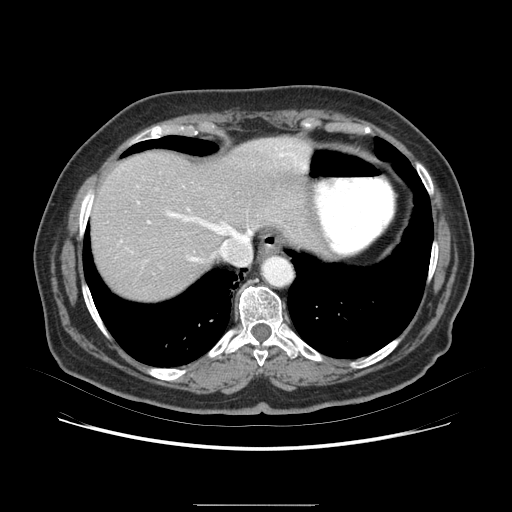
Contrast-enhanced abdominal CT (liver protocol), one axial slice; position 67 of 79 along the scan axis; 120 kVp; soft-tissue window (W 400 / L 40 HU); 2.5 mm slice thickness; 512 × 512 image matrix, field of view 380 × 380 mm. From the clinical record (not read from this slice): diagnosis: hepatocellular carcinoma (patient treated with transarterial chemoembolisation; whether this scan precedes or follows treatment is not stated here); TNM stage (as recorded): Stage-I; Child-Pugh class: A.
Structures marked on this image (semi-automatic segmentation, software-assisted and operator-edited):
- liver parenchyma outside the tumour (the mass and vessels are separate outlines, so this box may not span the whole liver): bounding box <96,150,332,279> (left, top, right, bottom; pixels)
- liver vessels: <152,216,160,232>